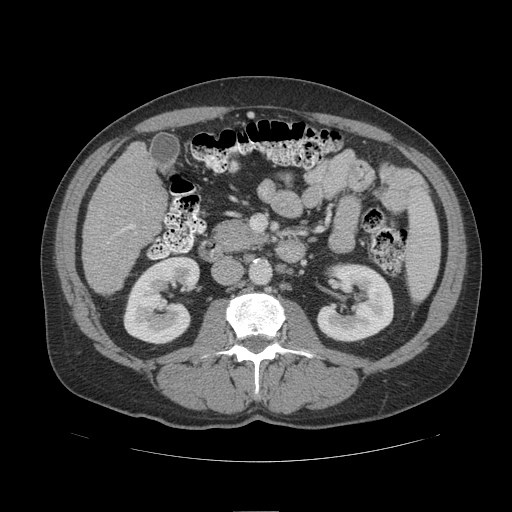
Contrast-enhanced abdominal CT (liver protocol), one axial slice; reconstruction kernel STANDARD; soft-tissue window (W 400 / L 40 HU); 512 × 512 image matrix, field of view 420 × 420 mm. From the clinical record (not read from this slice): diagnosis: hepatocellular carcinoma (patient treated with transarterial chemoembolisation; whether this scan precedes or follows treatment is not stated here); TNM stage (as recorded): Stage-IIIB; Child-Pugh class: A; tumour differentiation: poorly differentiated; tumour nodularity: multinodular.
Annotated regions visible in this slice (semi-automatic segmentation, software-assisted and operator-edited):
- liver parenchyma outside the tumour (the mass and vessels are separate outlines, so this box may not span the whole liver): bounding box [x1, y1, x2, y2] px = [82, 142, 166, 294]
- liver vessels: [120, 225, 133, 232]